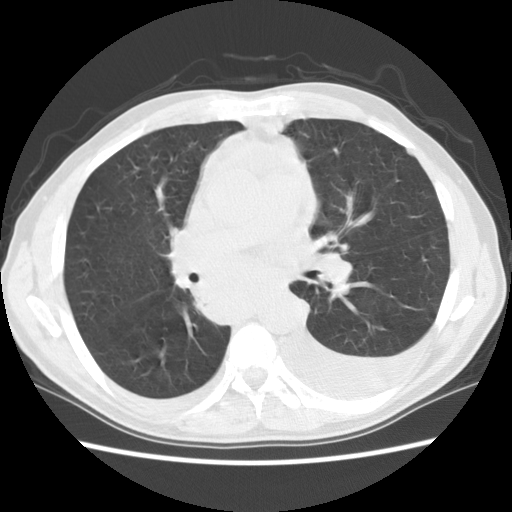
Chest CT (low-dose screening protocol), one axial image, baseline annual screen, lung window (W 1500 / L -600 HU), 2.5 mm slice thickness, 140 kVp, slice 54 of 135 in the series. Male, age 60 years at enrolment.
• Expert reader's lesion annotation, bounding box <175,239,300,330> (left, top, right, bottom; pixels).
• Screening reader's record for this exam: no non-calcified nodule ≥4 mm recorded.
• Official screen result: negative screen, significant abnormalities not suspicious for lung cancer.
• Later outcome: lung cancer diagnosed 12 days after this screen — squamous cell carcinoma, NOS, carina, poorly differentiated (G3), stage IV (AJCC 6th edition).